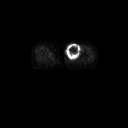
FDG PET of an extremity soft-tissue mass (from a PET/CT study), one axial slice; slice 37 of 91 in the series (ordered by position); 128 × 128 image matrix, field of view 700 × 700 mm. Patient: female, 74 years. From the clinical record (not read from this slice): histological type: pleomorphic leiomyosarcoma; grade: high; site of the primary tumour: left thigh.
Outlined on this slice (expert contour drawn on MRI and transferred to this co-registered scan by the dataset authors):
- gross tumour volume including surrounding oedema: box from (x=65, y=42) to (x=82, y=61) px
- gross tumour volume (mass): (x=65, y=42)–(x=81, y=60)